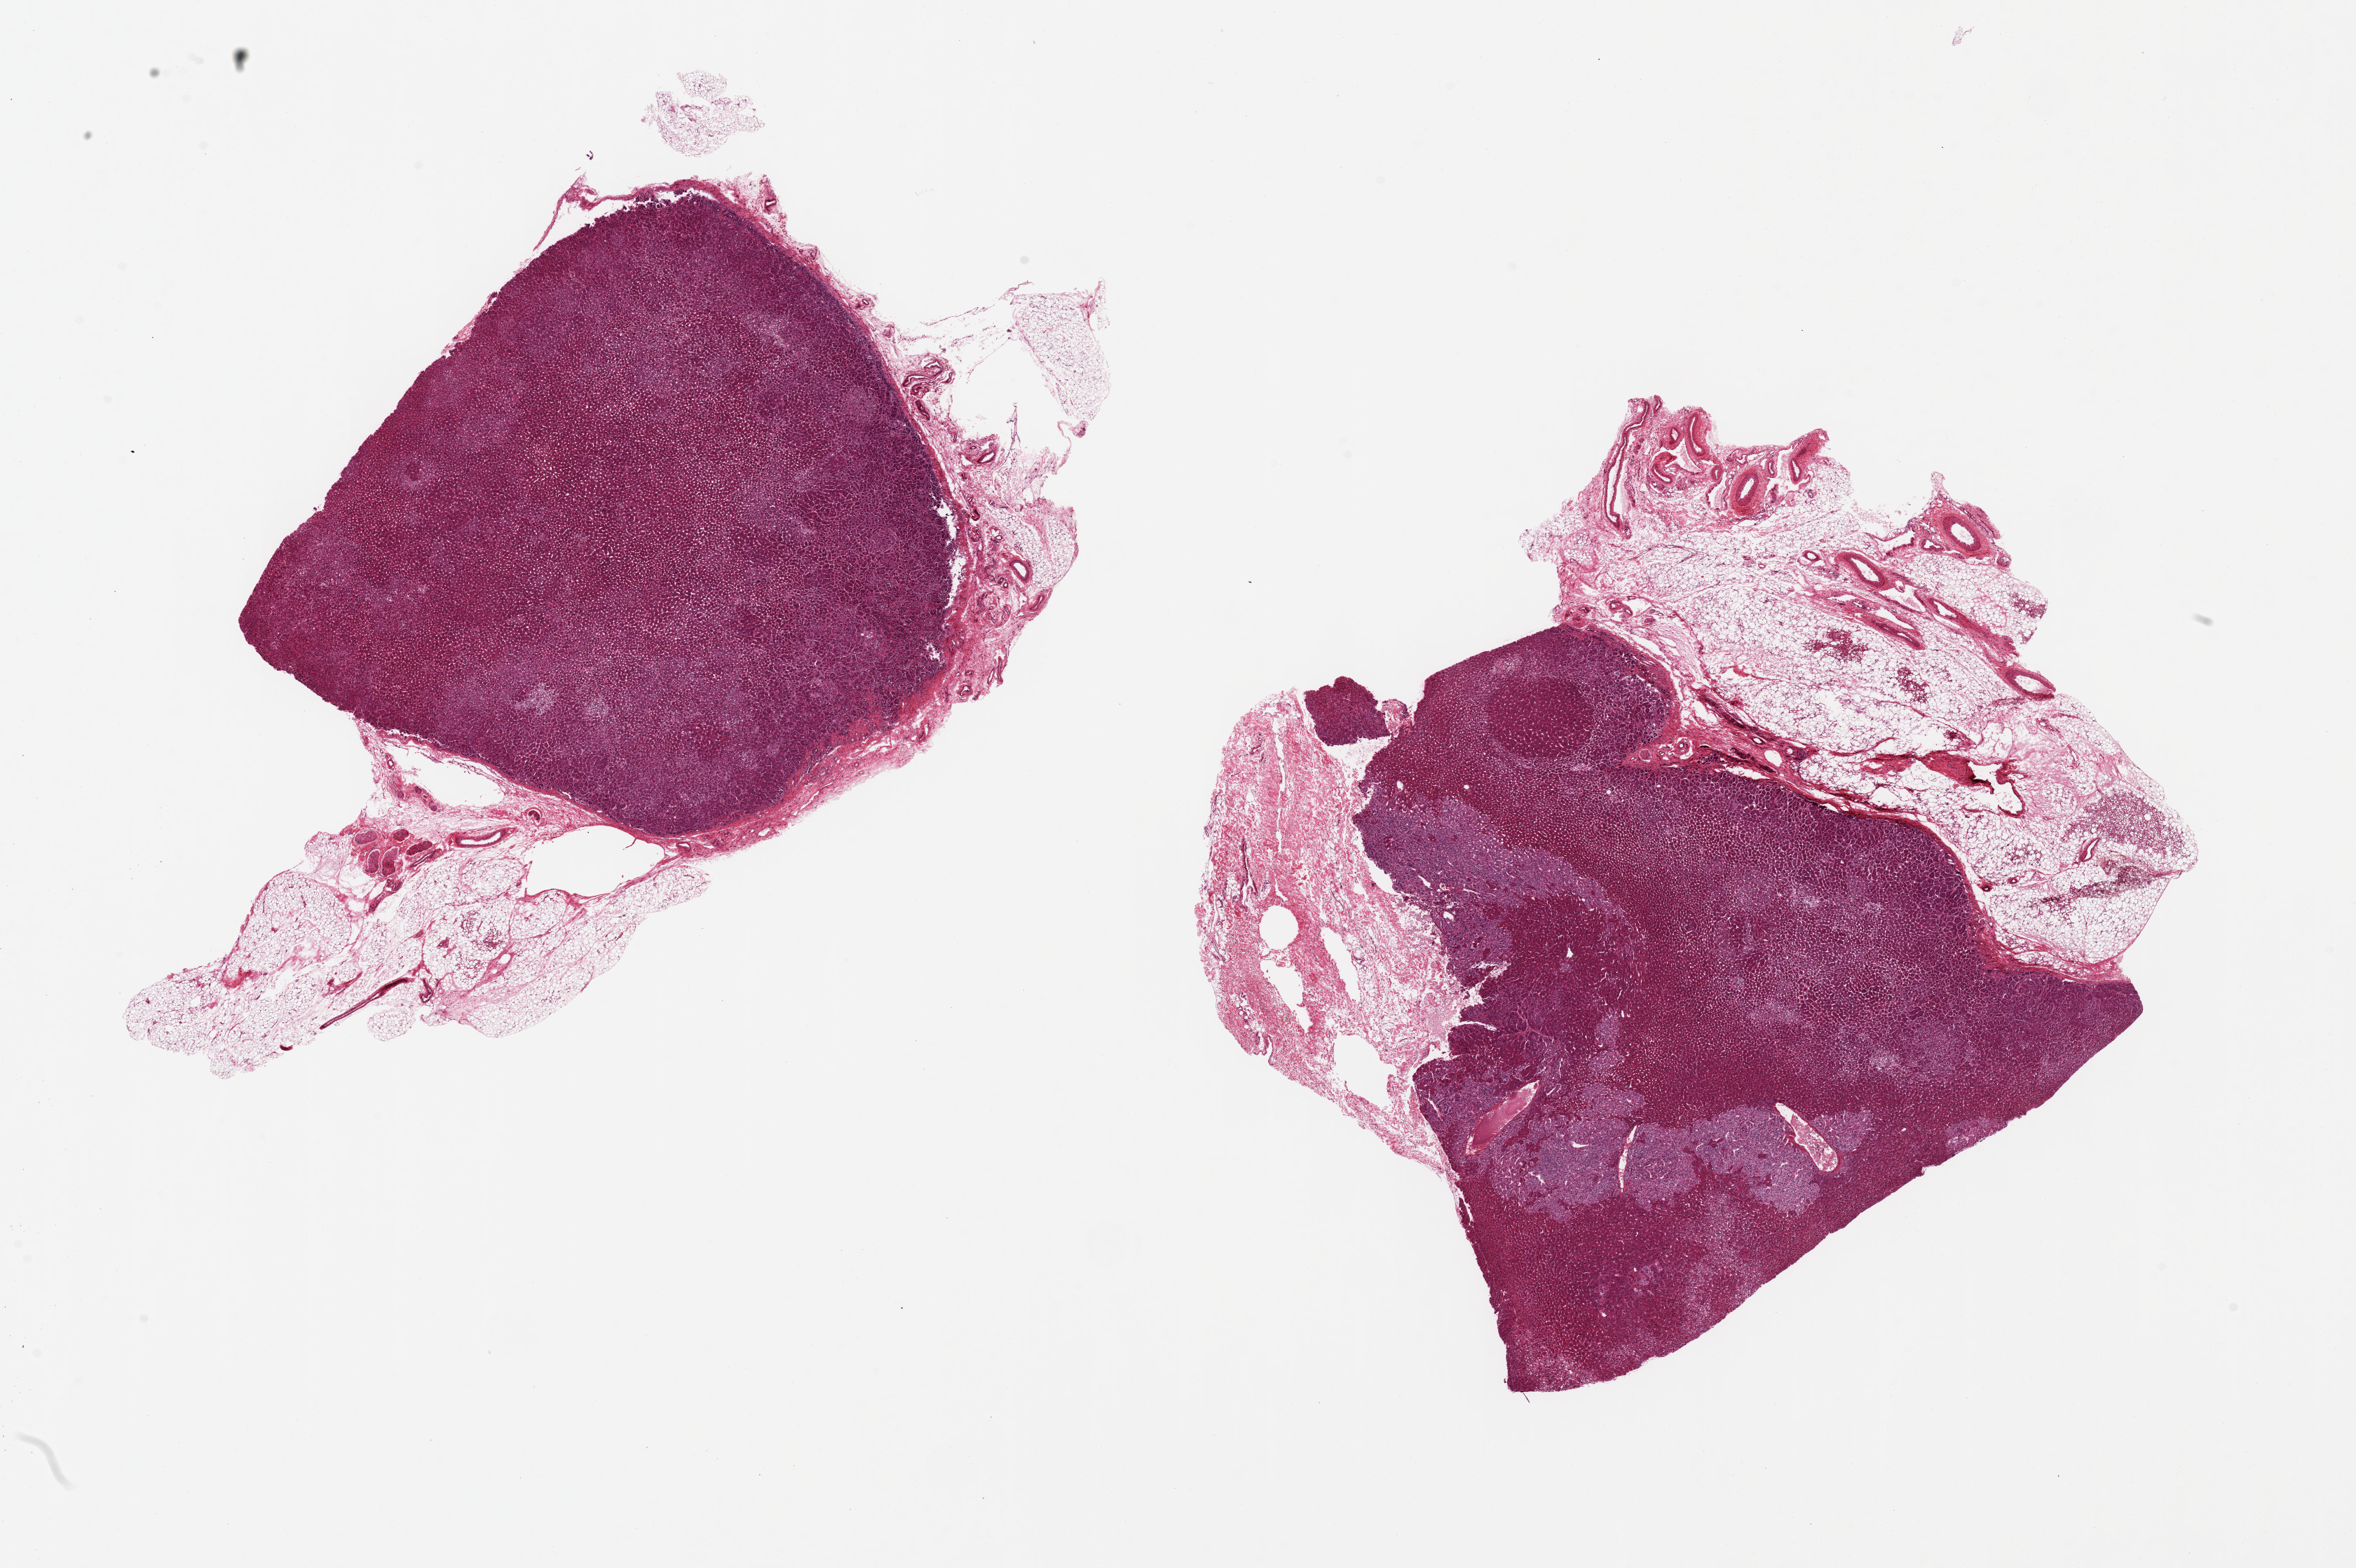
Digitized H&E-stained section — shown as a low-resolution overview of the whole scanned area (about 26.6 x 17.7 mm, acquisition: 20x scan); PAXgene-fixed paraffin-embedded (PFPE) section; sampled site (target tissue): adrenal gland; donor tissue sample. Female donor.
• pathologist's review note for this sample: 2 pieces 7x7 & 10x8 mm; cortex and medulla; one with ~40% peripheral adipose and other with ~20% adipose